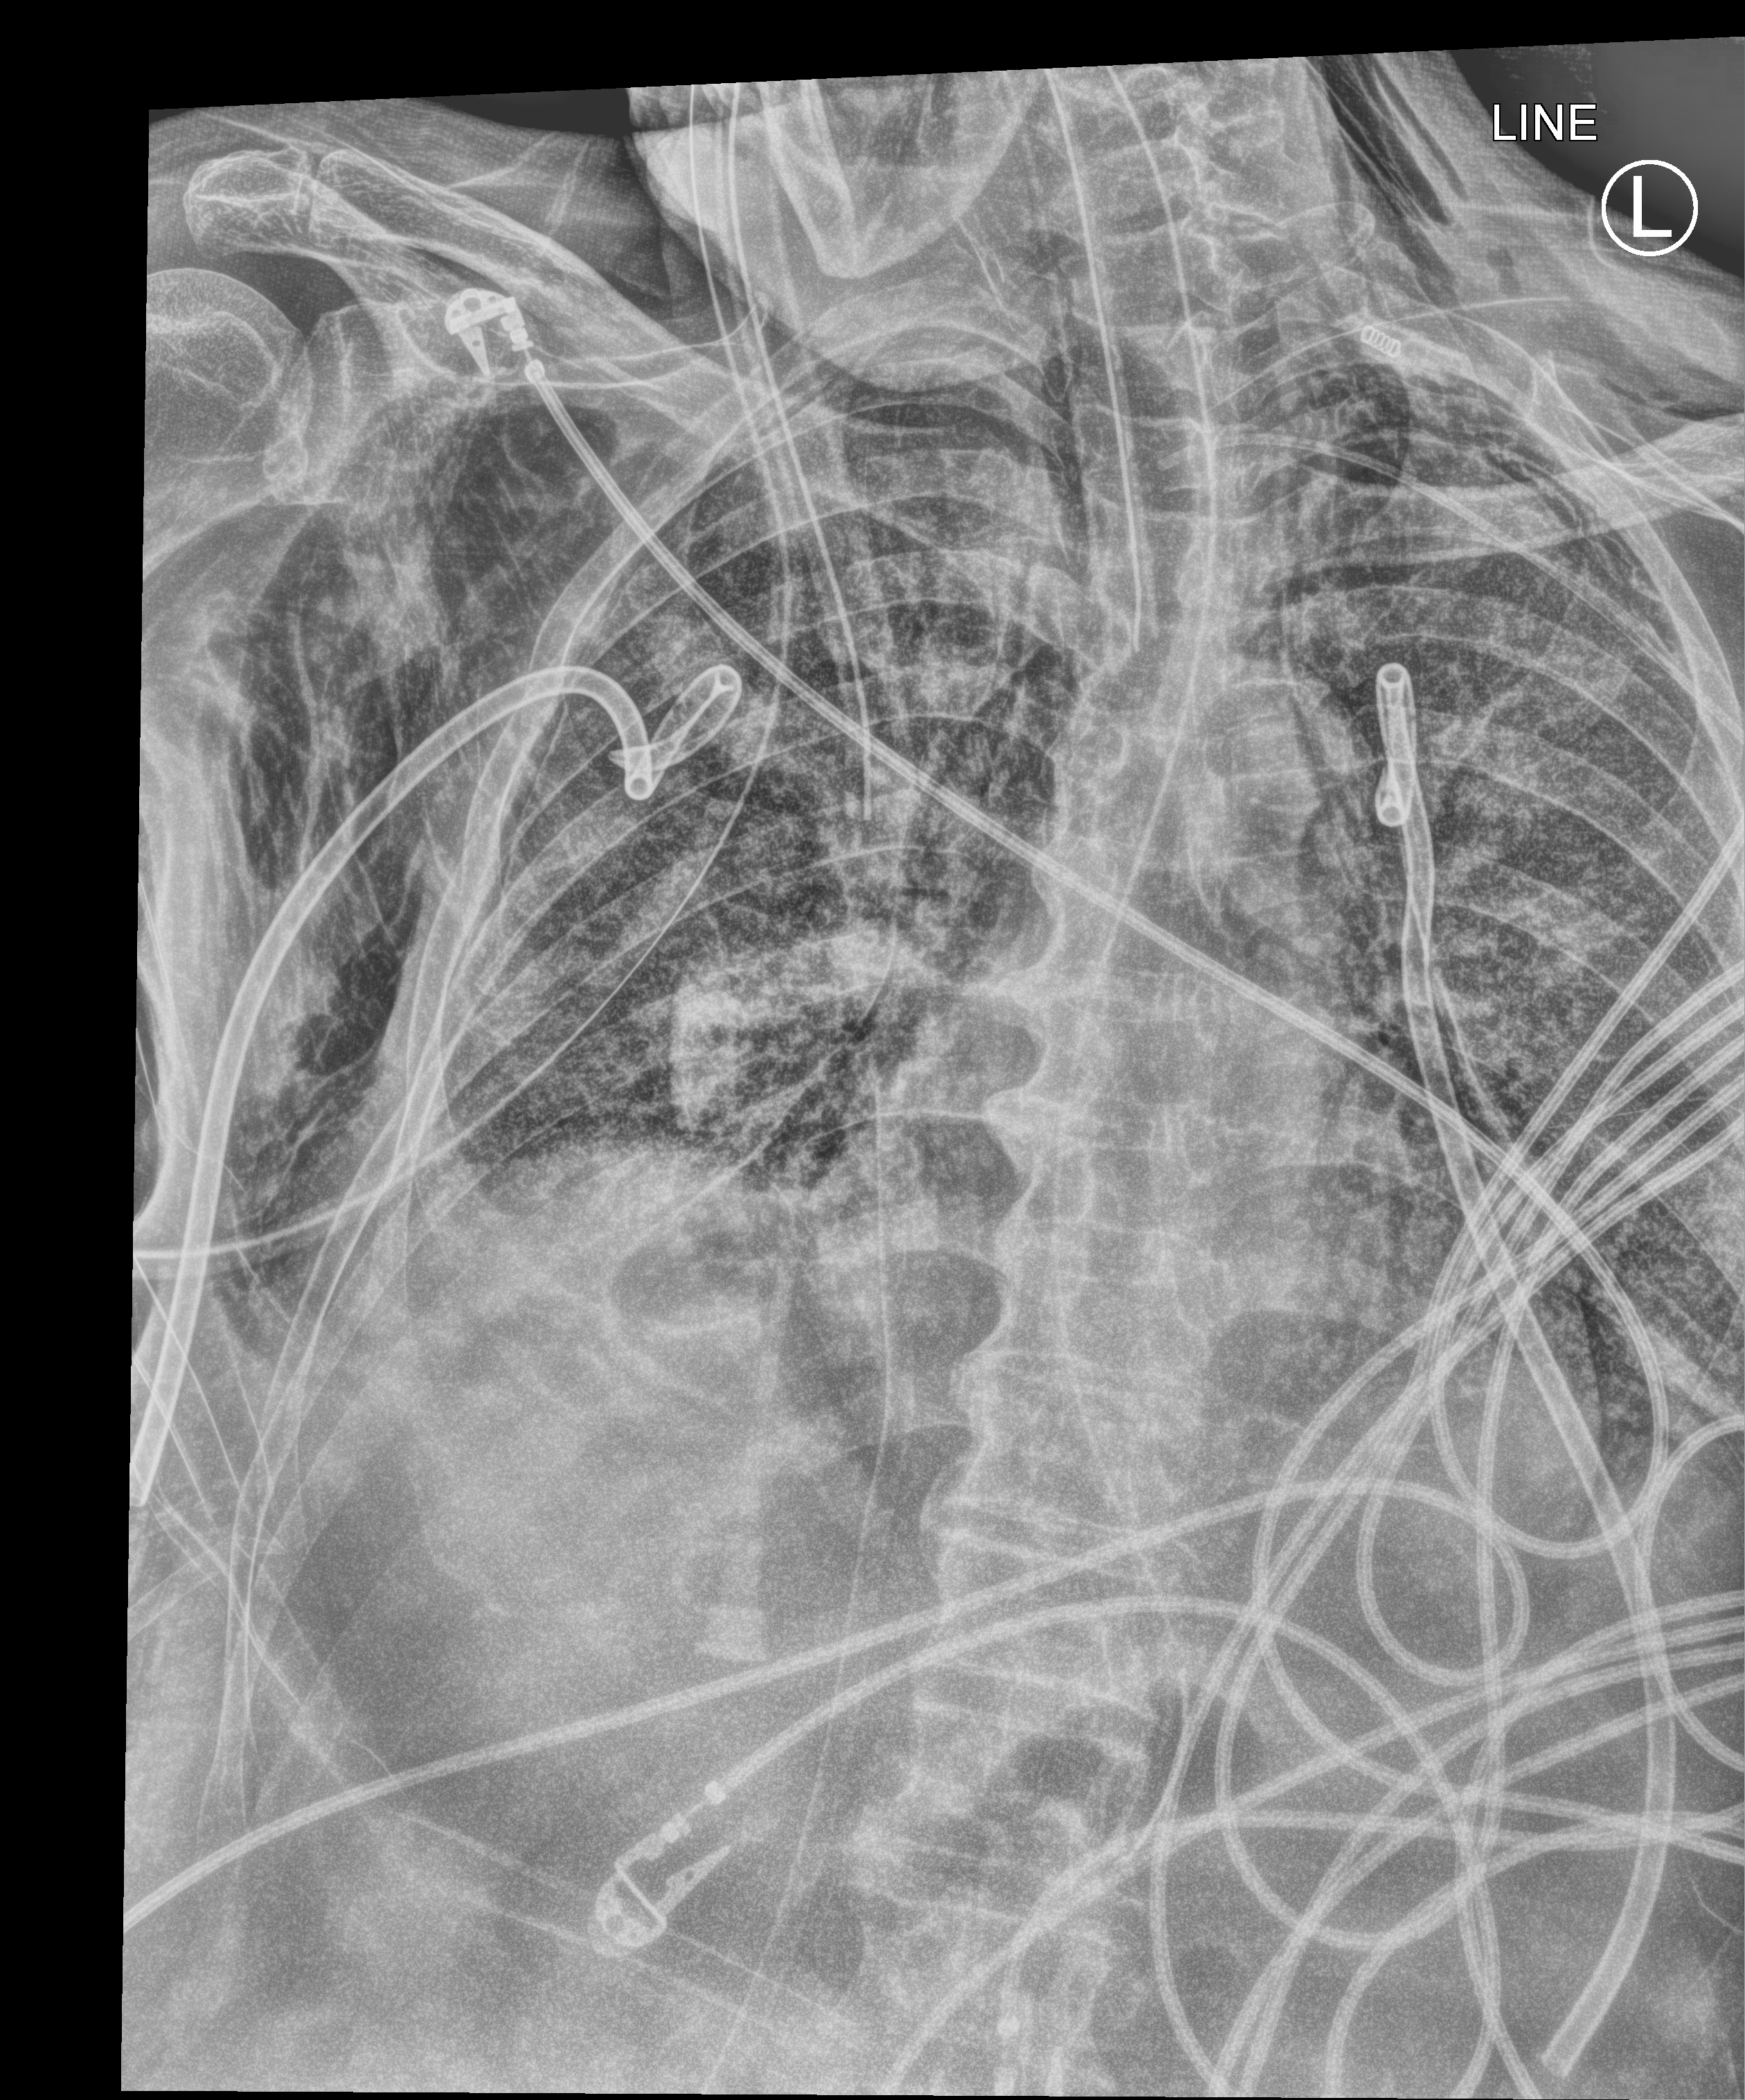
Bedside chest radiograph (computed radiography), anteroposterior (AP) projection. Patient hospitalised with COVID-19; male, aged 75–90 years.
Admission-level facts for this patient (not findings on this image; timing relative to this image not recorded): mechanically ventilated during this hospital stay: yes; admitted to intensive care during this hospital stay: yes; hypertension (admission record): yes.